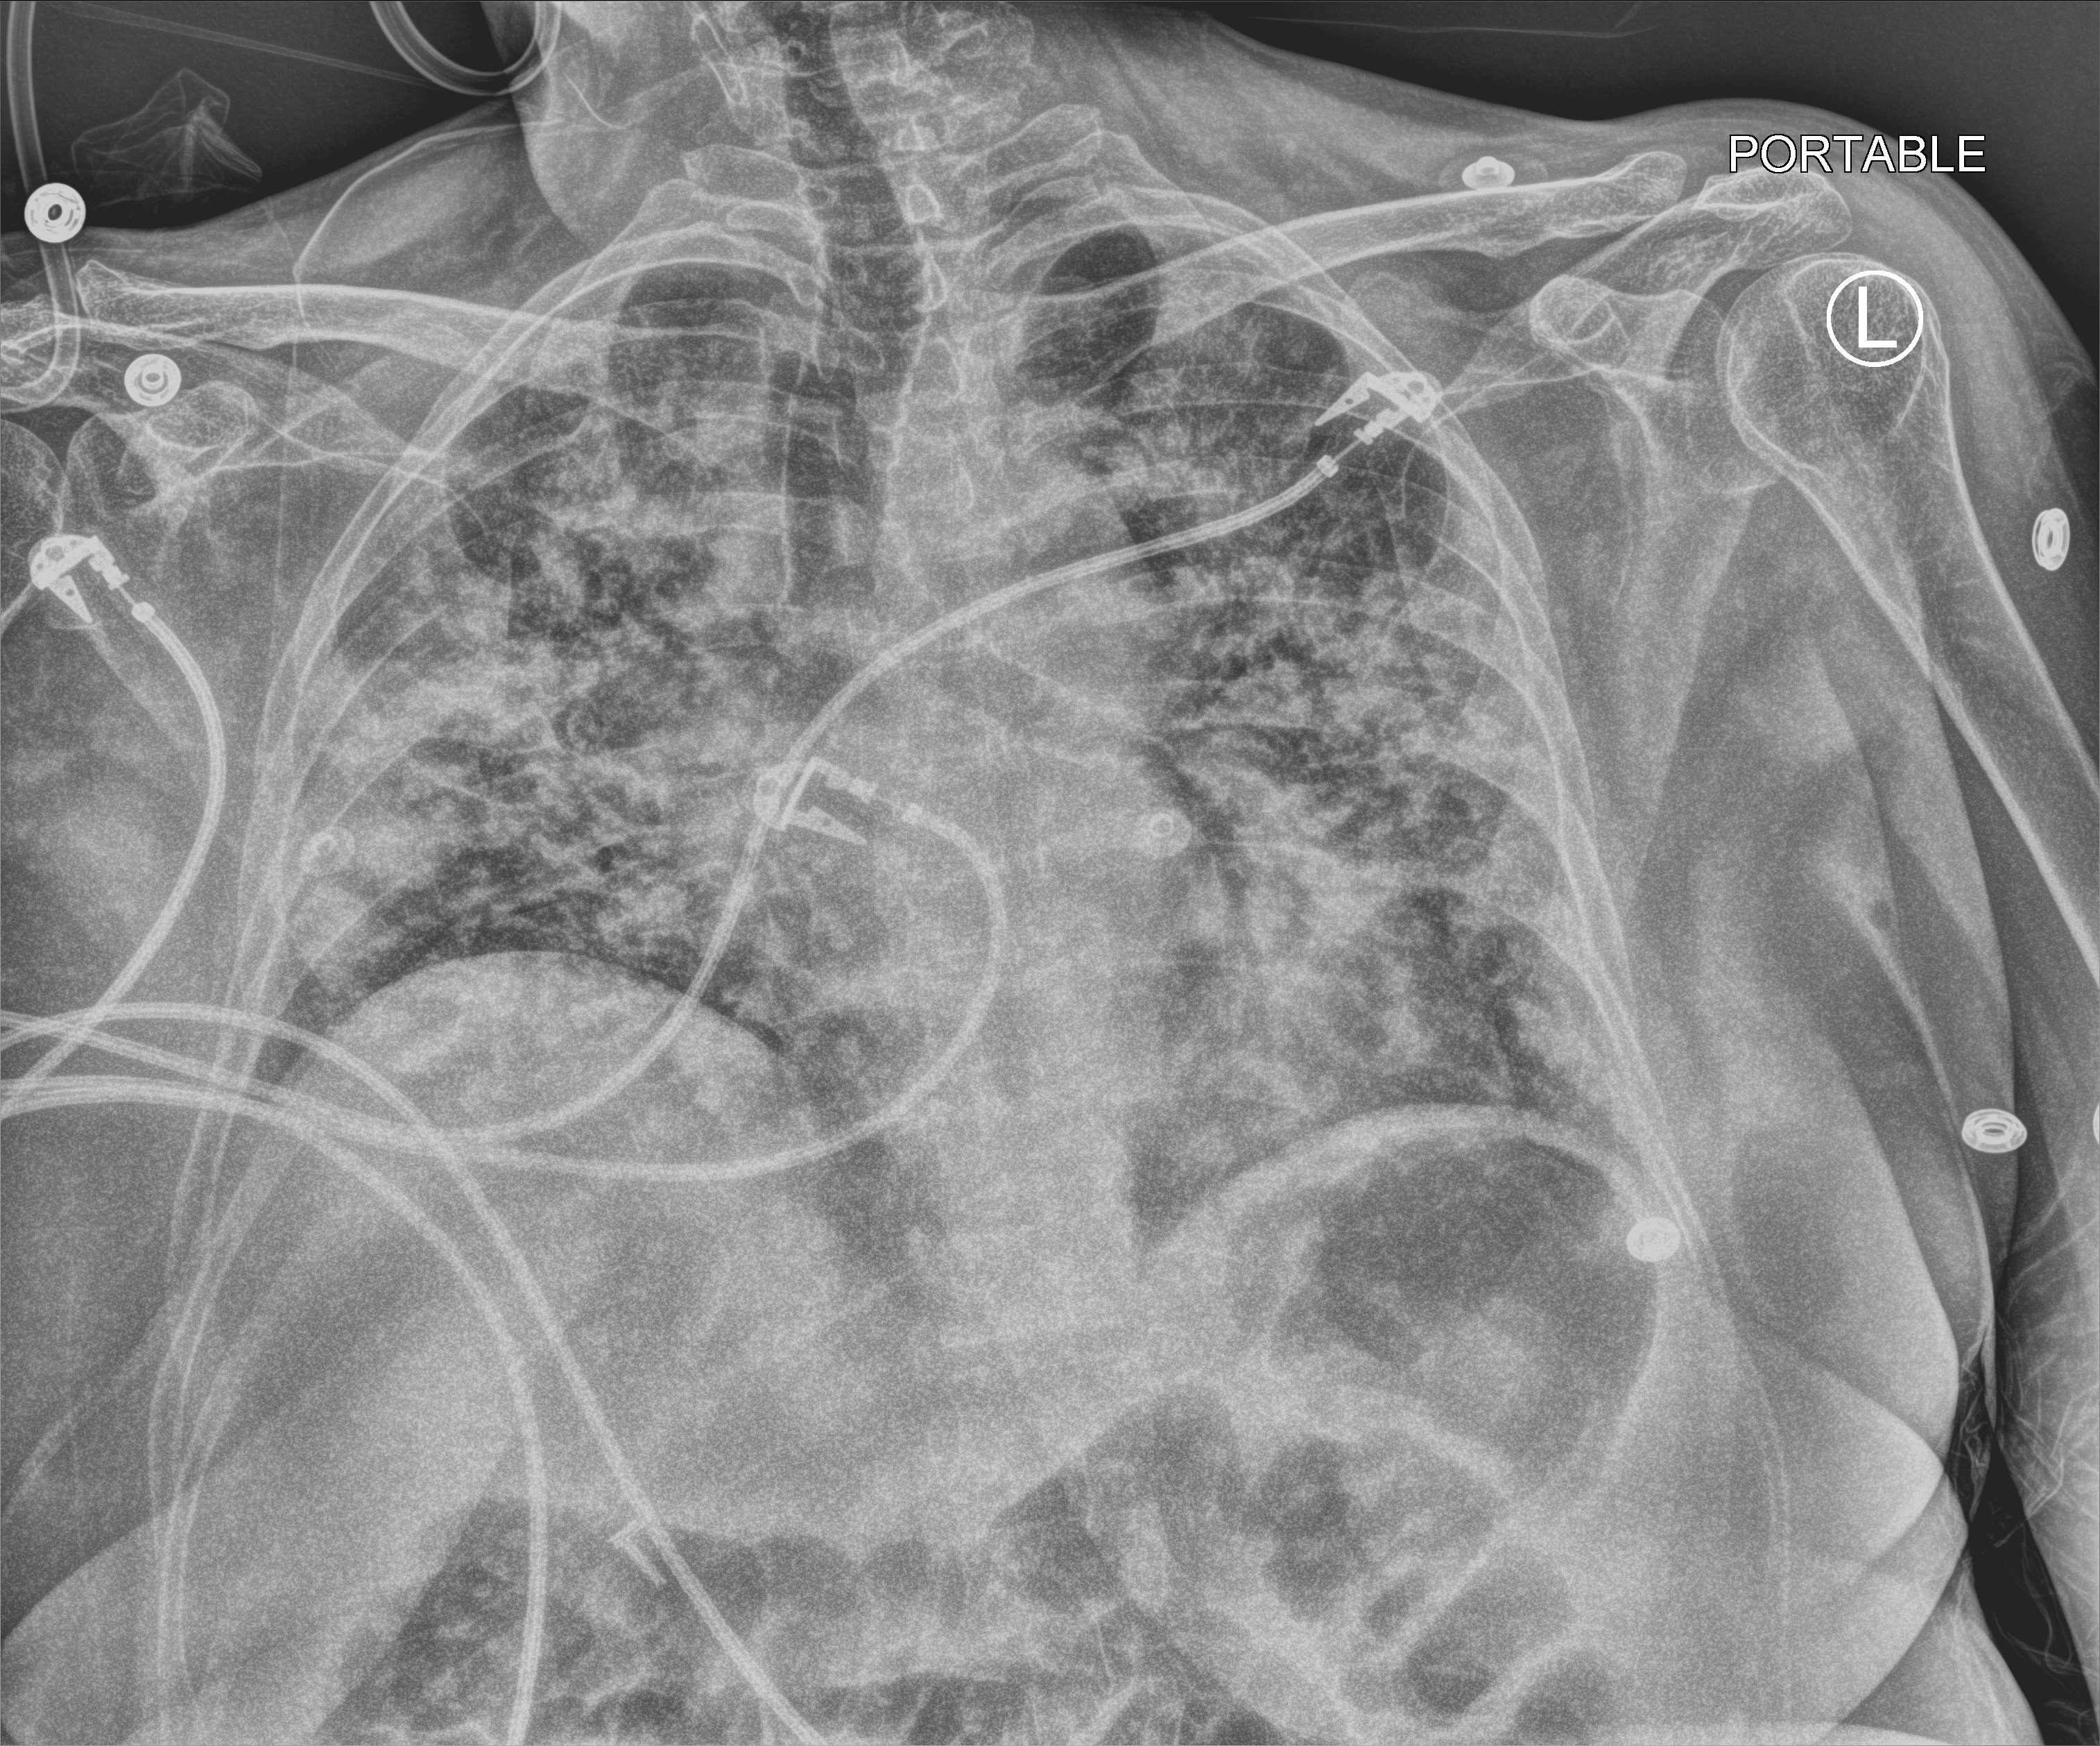
Chest X-ray (portable); anteroposterior (AP) projection. Patient hospitalised with COVID-19; female, aged 18–59 years.
Admission-level facts for this patient (not findings on this image; timing relative to this image not recorded): admitted to intensive care during this hospital stay: yes; hypertension (admission record): no.